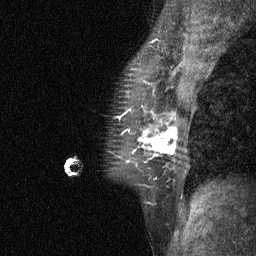
Breast MRI (dynamic contrast-enhanced), one sagittal slice; position 43 of 64 along the scan axis; dynamic contrast-enhanced study with each time point stored as its own series, time point 3 of 4 at this slice position (ordered by acquisition time); 1.5 T; TE 4.8 ms, TR 27 ms; 2 mm slice thickness; 256 × 256 image matrix, field of view 180 × 180 mm. Patient: female, 44 years. Case-level facts recorded for this patient, not image findings: setting: breast cancer imaged before/during neoadjuvant chemotherapy; receptor status: HR-positive, HER2-negative.
Structures marked on this image (semi-automatically segmented with operator editing):
- analysis volume of interest (the breast-tissue region the enhancement analysis was run in; not a lesion): bounding box <115,117,185,188> (left, top, right, bottom; pixels)
- tumour enhancement mask (voxels above the 90 % enhancement threshold inside the analysis volume of interest): <145,118,178,155>